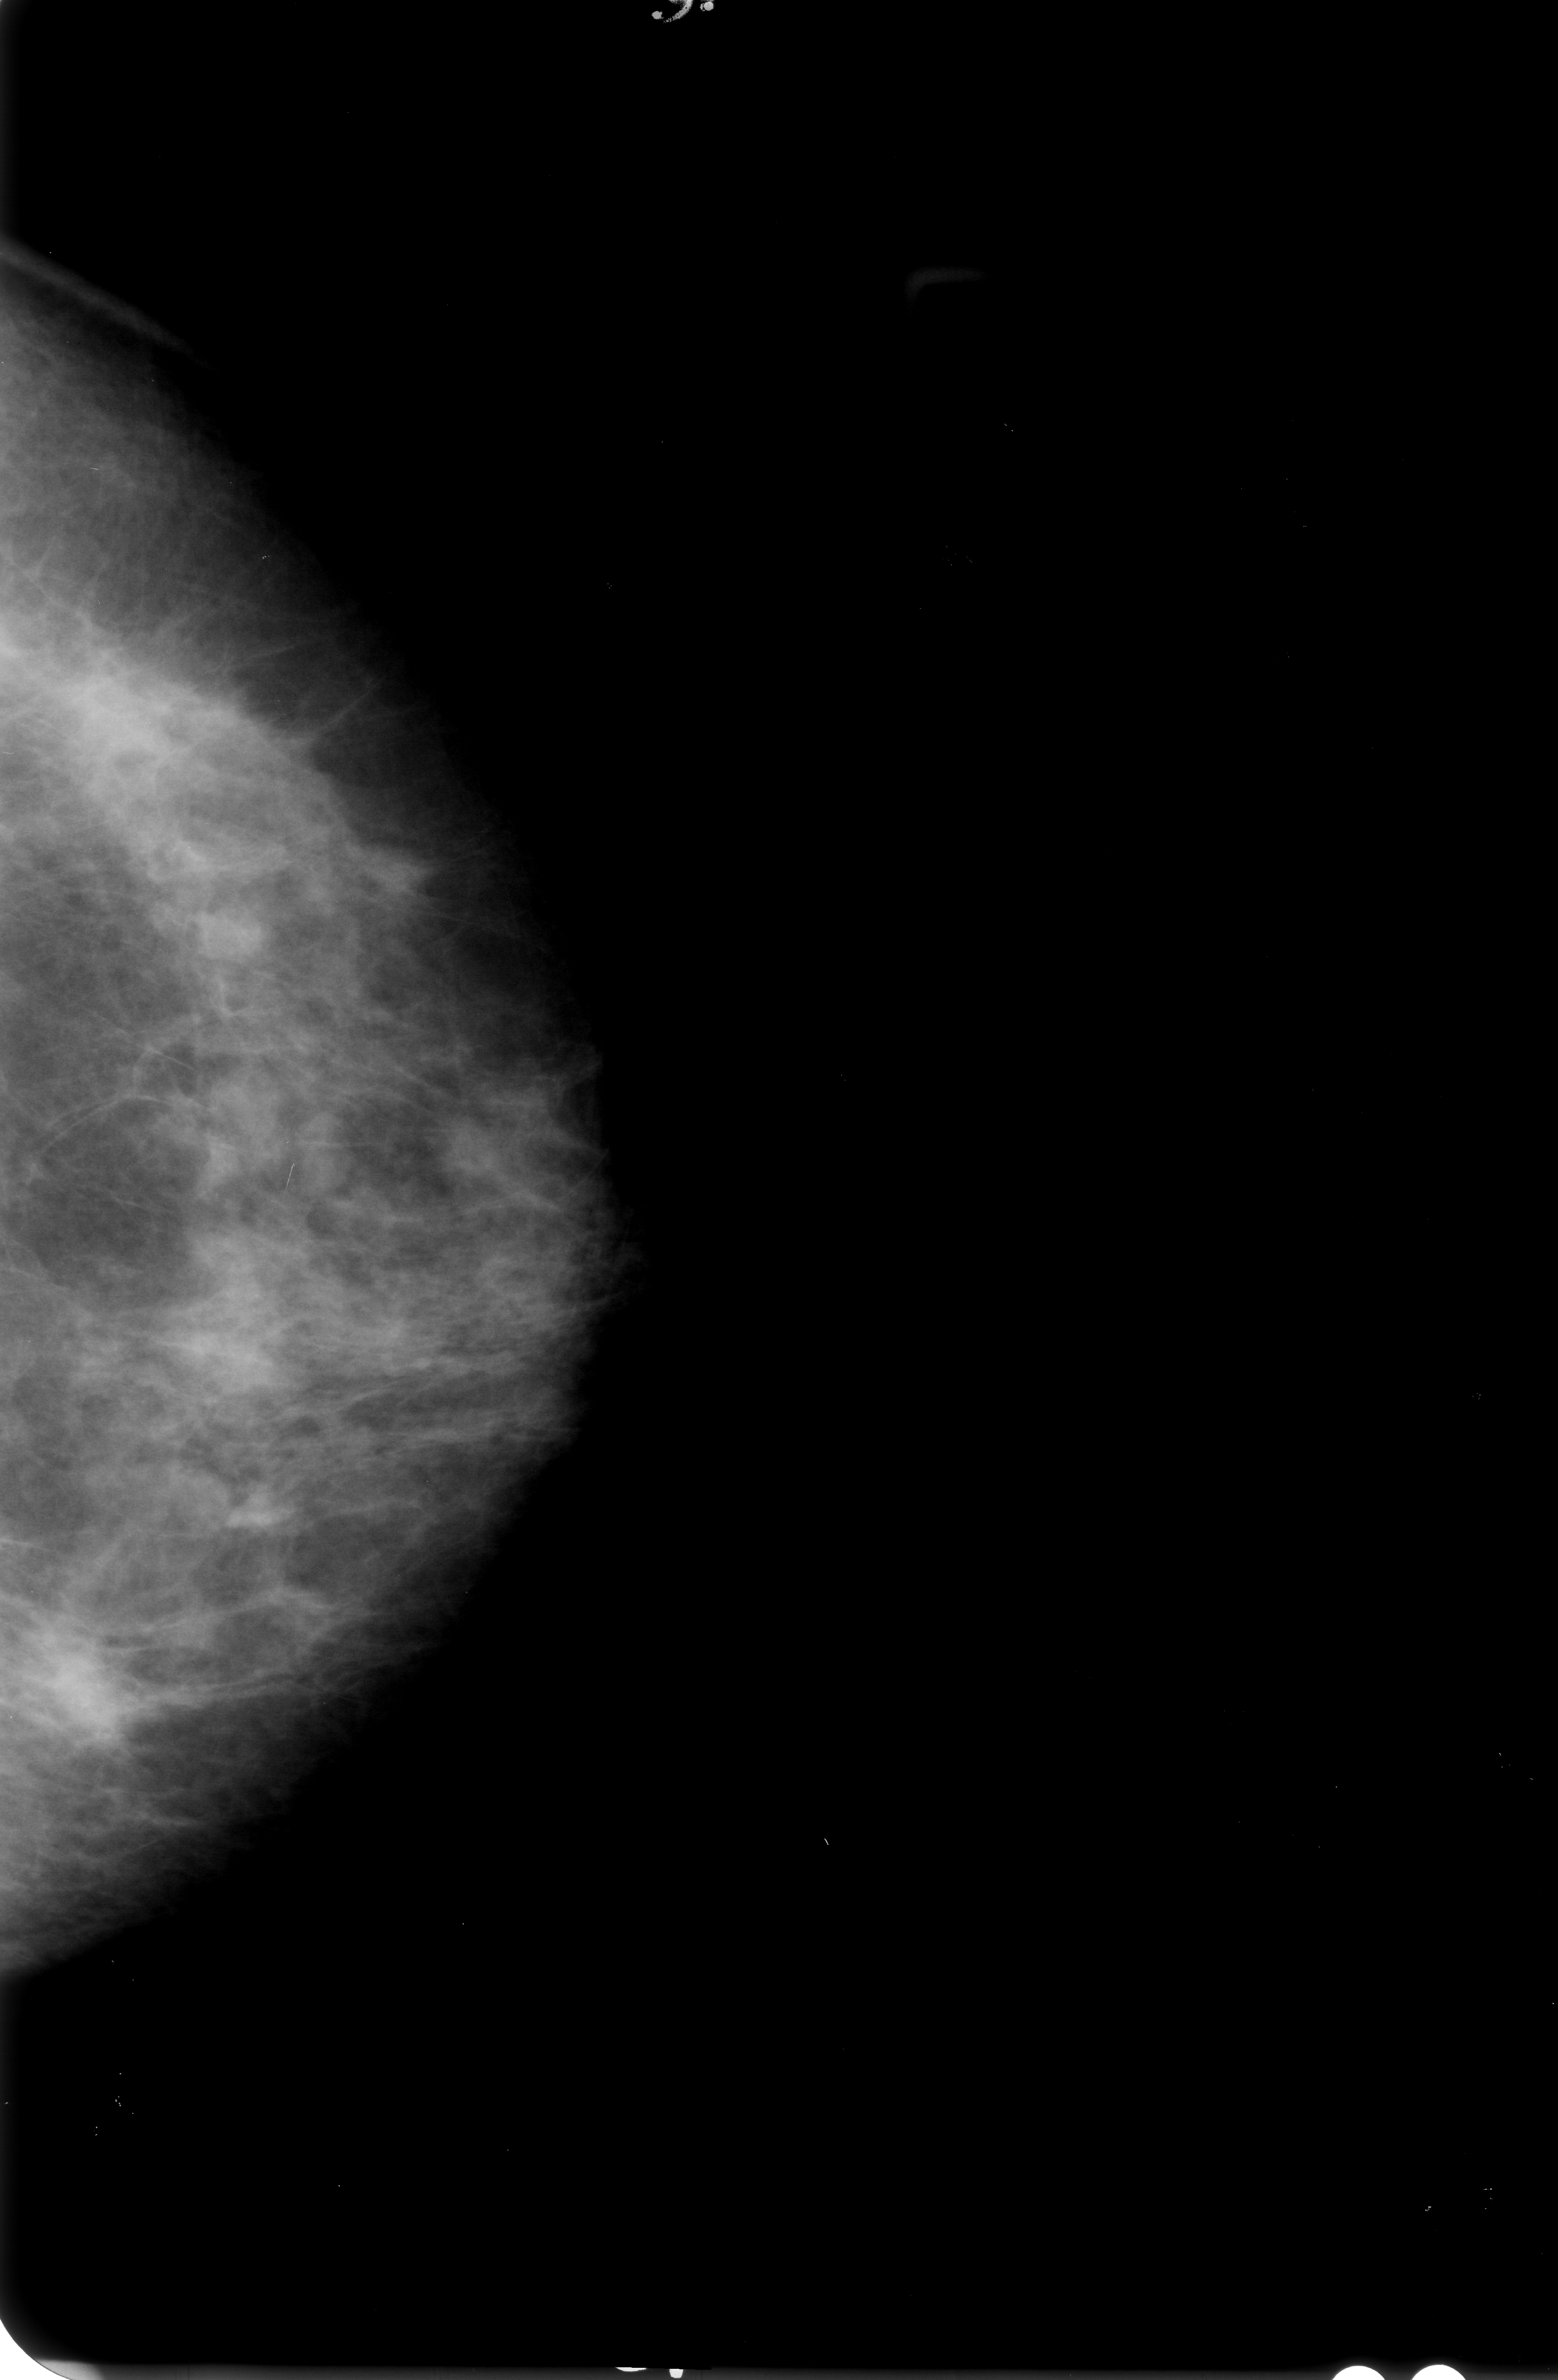
Mammogram (digitized film). Left breast. CC view. 1558 × 2380 image matrix.
Expert-marked regions of interest on this film, with their recorded descriptors:
- calcifications, morphology pleomorphic, distribution clustered; BI-RADS assessment category 4; subtlety rating 3 on a 1 (subtle) to 5 (obvious) scale; pathology result (as recorded, not read from the image): malignant: box from (x=44, y=1619) to (x=156, y=1759) px